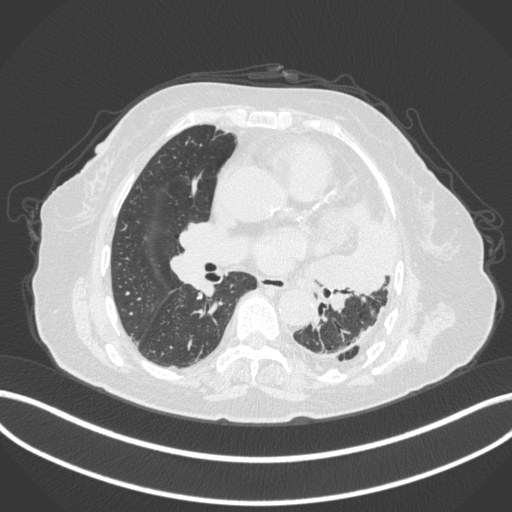
Chest CT, one axial slice. Lung window (W 1500 / L -600 HU). 1 mm slice thickness. 512 × 512 image matrix, field of view 400 × 400 mm. Female patient, age 75 years. From the clinical record (not read from this slice): clinical TNM (as recorded): T3 N3 M1.
Annotated regions visible in this slice (bounding box drawn by a radiologist):
- lung tumour (recorded histology: adenocarcinoma): bounding box <311,193,398,304> (left, top, right, bottom; pixels)